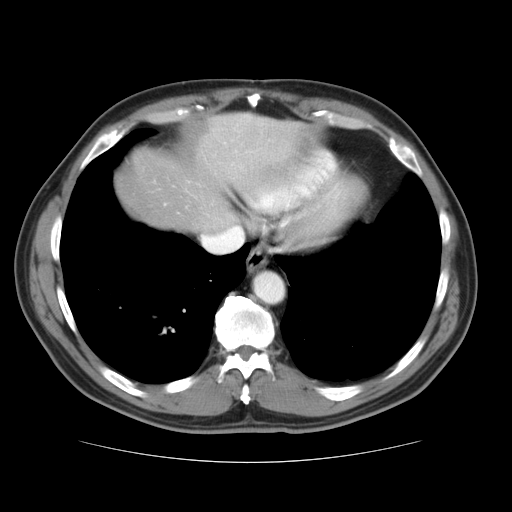
Contrast-enhanced abdominal CT, one axial slice; slice 33 of 37 in the series (ordered by position); intravenous contrast given; soft-tissue window (W 400 / L 40 HU); 5 mm slice thickness; 512 × 512 image matrix, field of view 374 × 374 mm. Male patient, age 66 years. From the clinical record (not read from this slice): diagnosis: colorectal cancer liver metastases, imaged before liver resection; multiple liver metastases: yes.
Annotated regions visible in this slice (outlined manually by an expert reader):
- liver: bounding box [x1, y1, x2, y2] px = [117, 113, 317, 236]
- planned liver remnant (the part of the liver to remain after resection): [125, 116, 317, 236]